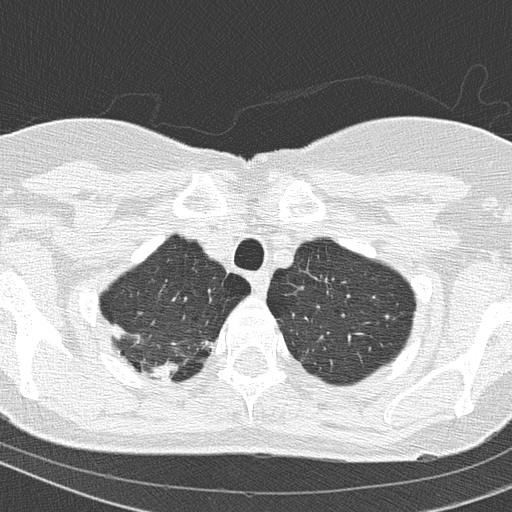
Axial slice from a low-dose chest CT screening exam, first (baseline) screen, lung window (W 1500 / L -600 HU), lung (sharp) reconstruction kernel (B50f), slice 20 of 154 in the series. Female participant, aged 67 years at enrolment.
Lesion marked by an expert reader, box from (x=126, y=341) to (x=189, y=389) px. Screening reader's record for this exam (one nodule recorded; not confirmed to be the boxed lesion): non-calcified nodule or mass ≥4 mm, right upper lobe, 15 × 14 mm, spiculated (stellate) margins, soft tissue attenuation. Official screen result: positive, change unspecified: nodule(s) >= 4 mm or enlarging nodule(s), mass(es), or other non-specific abnormalities suspicious for lung cancer. Lung cancer was diagnosed 63 days after this screen: adenocarcinoma, NOS, right upper lobe, moderately differentiated (G2), stage IA (AJCC 6th edition), 14 mm at pathology.